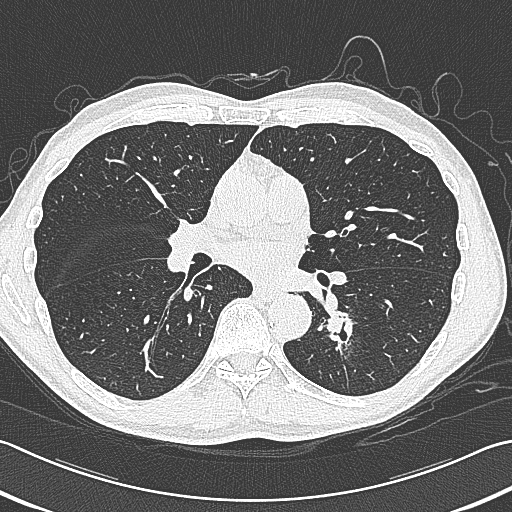
Axial slice from a low-dose chest CT screening exam; baseline screening round; lung window (W 1500 / L -600 HU); 1 mm slice thickness; slice 171 of 354 in the series. Male, age 59 years at enrolment.
Expert reader's lesion annotation, bounding box (x1, y1, x2, y2) in pixels: (313, 294, 375, 353). Screening reader's record for this exam (one nodule recorded; not confirmed to be the boxed lesion): non-calcified nodule or mass ≥4 mm, left lower lobe, 15 × 15 mm, smooth margins, soft tissue attenuation. Participant outcome: lung cancer diagnosed 17 days after this screen — squamous cell carcinoma, large cell, nonkeratinizing, NOS, left lower lobe, poorly differentiated (G3), stage IB (AJCC 6th edition), 31 mm at pathology.